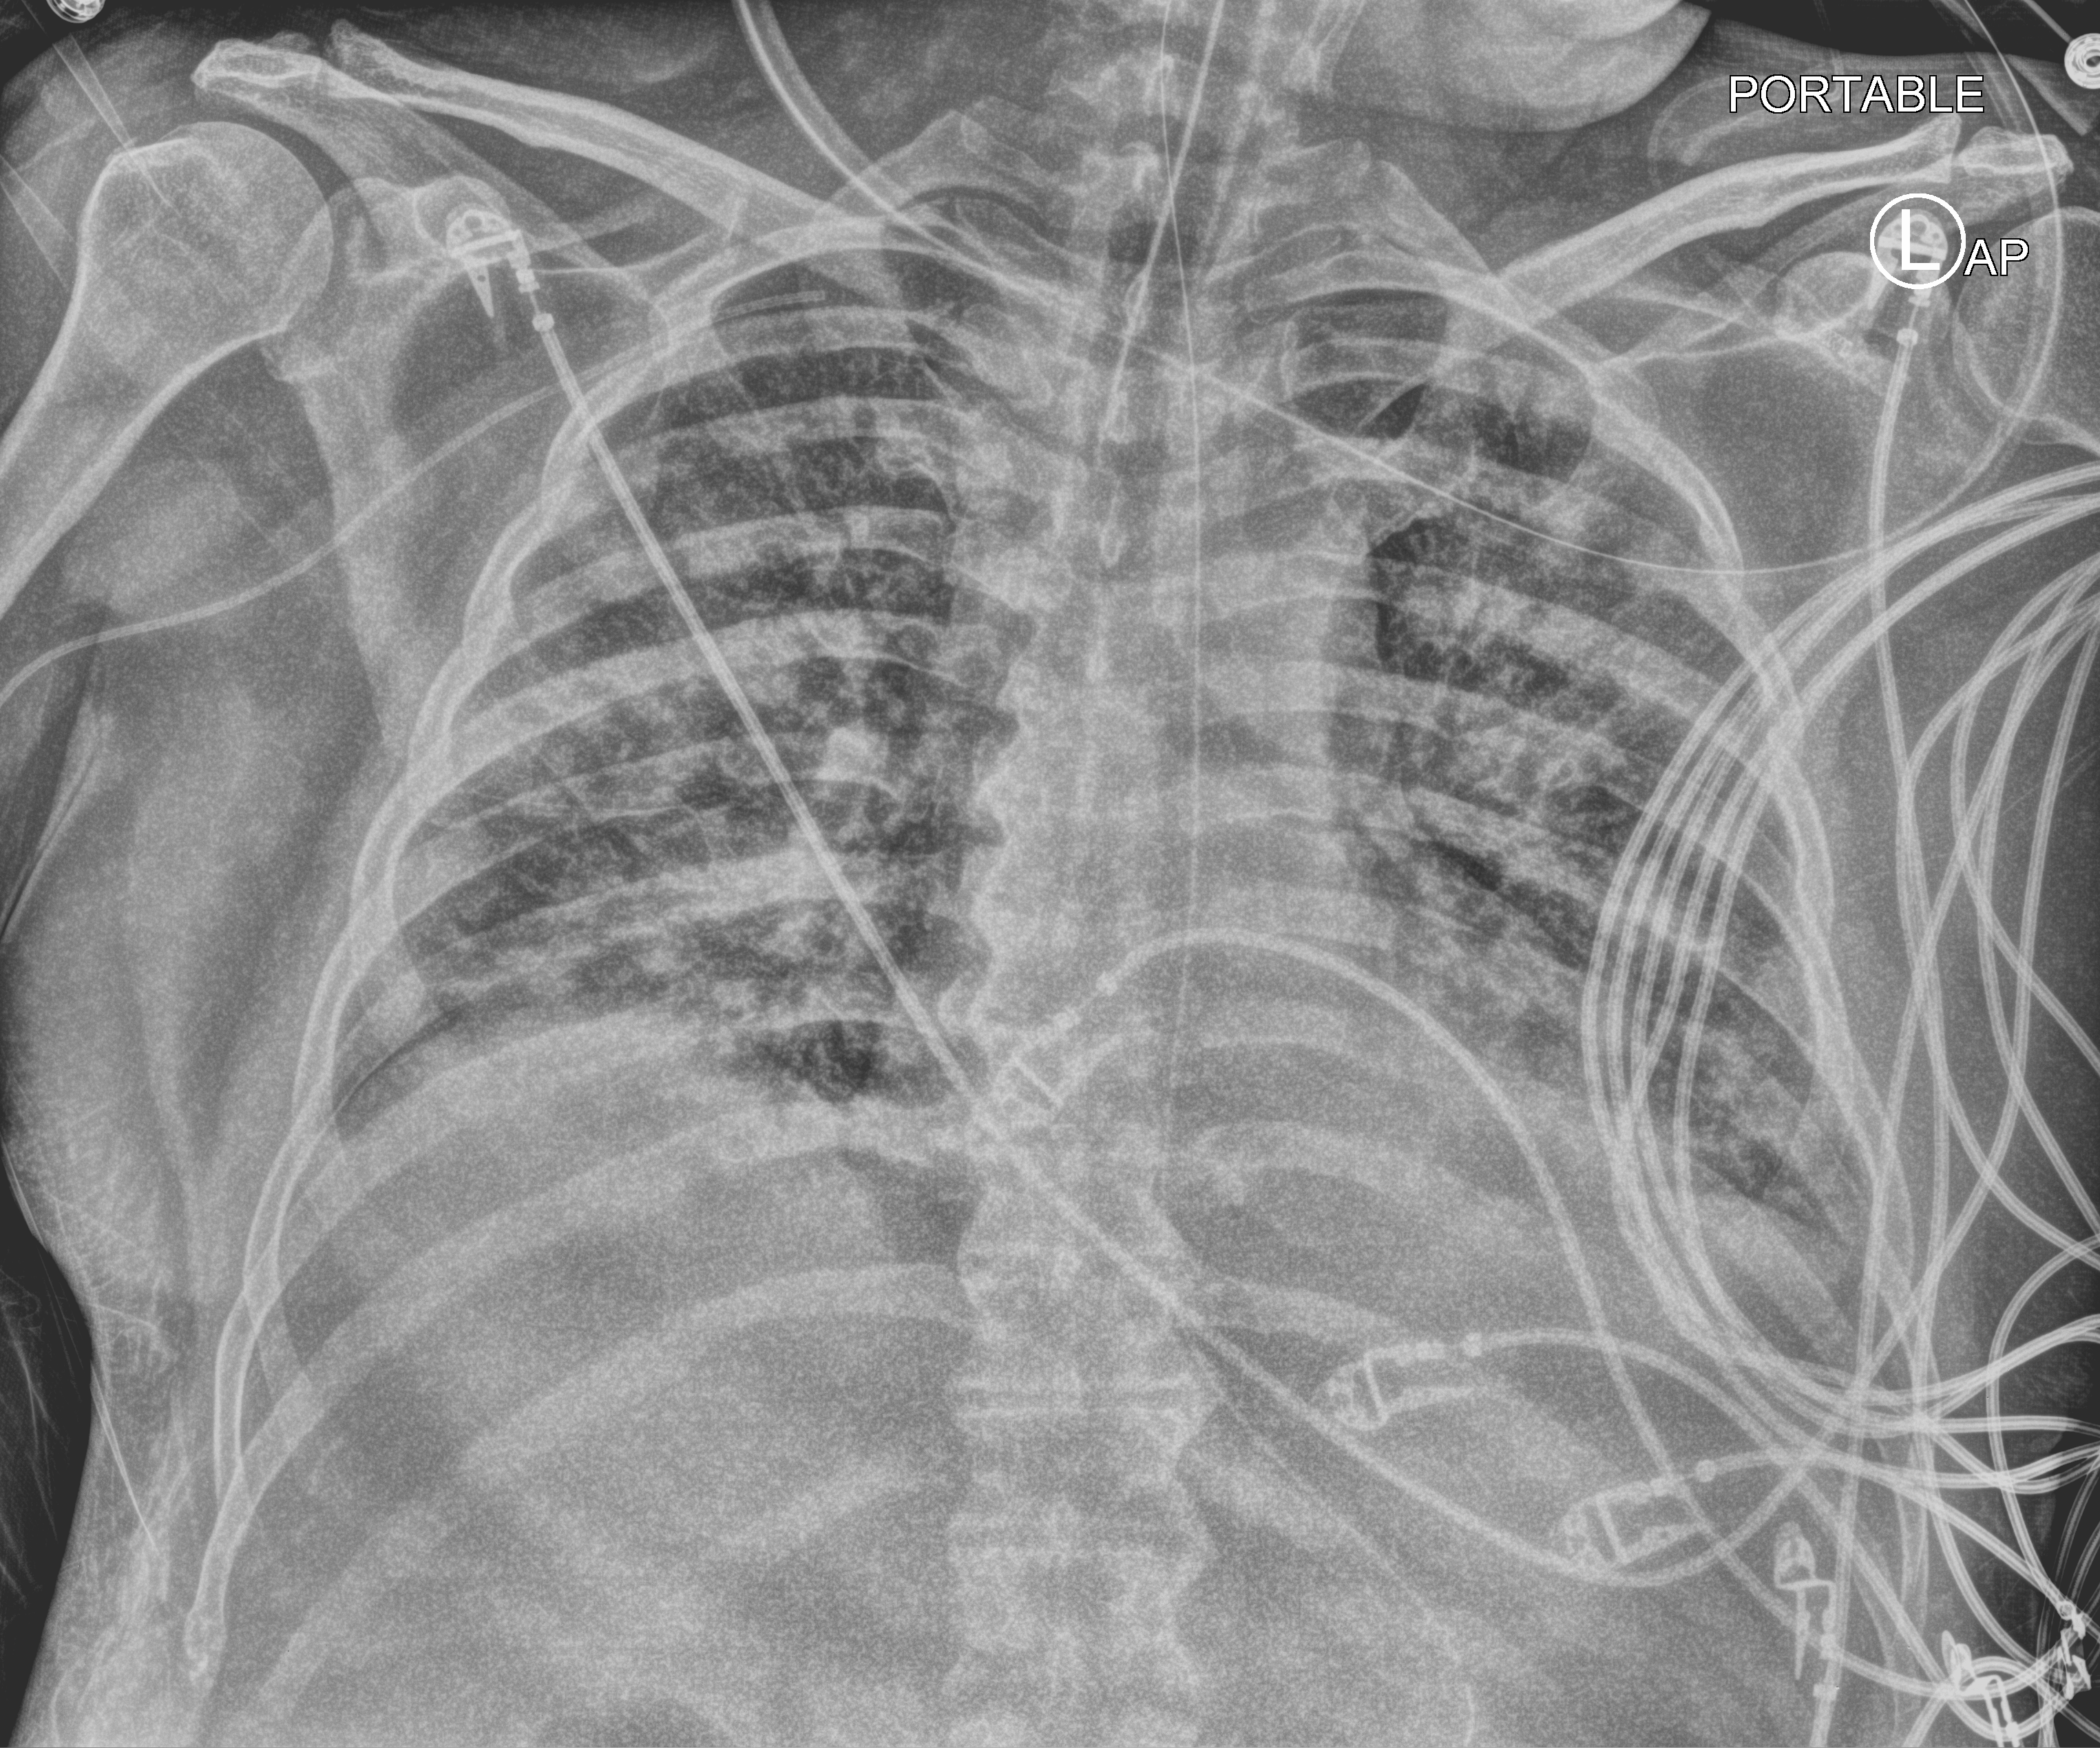
Bedside chest radiograph (computed radiography). Patient hospitalised with COVID-19; male, aged 18–59 years.
Hospital-stay facts (about this admission, not read from this image; timing relative to this image not recorded):
- mechanically ventilated during this hospital stay: yes